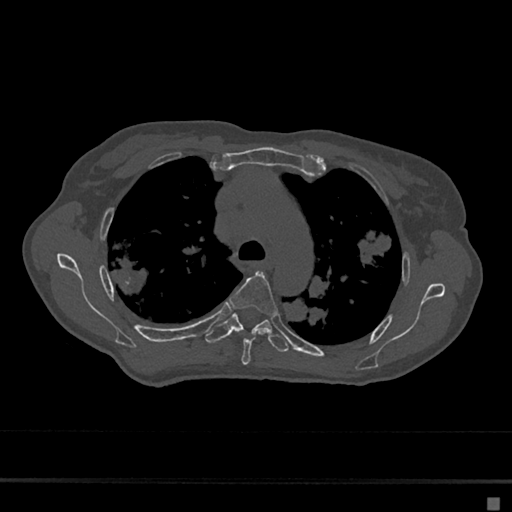
CT including the spine, one axial slice. Slice 484 of 797 in the series (ordered by position). Reconstruction kernel Br40s/3. 120 kVp. Bone window (W 1800 / L 400 HU). 512 × 512 image matrix, field of view 360 × 360 mm. Female patient, age 68 years. Case-level facts recorded for this patient, not image findings: primary cancer: renal.
Outlined on this slice (semi-automatic segmentation, software-assisted and operator-edited):
- T4 vertebra: box from (x=228, y=271) to (x=278, y=365) px
- T5 vertebra: (x=205, y=310)–(x=289, y=352)